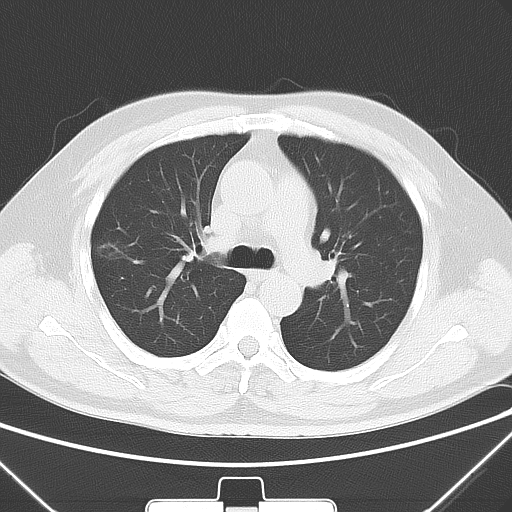
Chest CT, one axial slice; slice 41 of 64 in the series (ordered by position); lung window (W 1500 / L -600 HU); 512 × 512 image matrix, field of view 350 × 350 mm. Patient: male, 58 years. Case-level facts recorded for this patient, not image findings: clinical TNM (as recorded): T1c N0 M0; histopathological grade: G2.
Annotated regions visible in this slice (rectangle marked by the reading radiologist):
- lung tumour (recorded histology: adenocarcinoma): box from (x=92, y=233) to (x=133, y=269) px